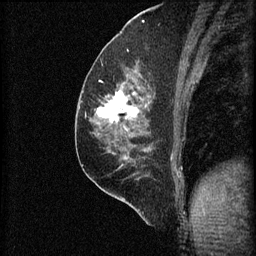
Breast MRI (dynamic contrast-enhanced), one sagittal slice; slice 33 of 60 in the series (ordered by position); 3 images stored at this slice position (order not interpretable as contrast timing); 1.5 T; TE 4.2 ms, TR 8.2 ms; 2 mm slice thickness; 256 × 256 image matrix, field of view 180 × 180 mm. Patient: female, 59 years.
Outlined on this slice (semi-automatic segmentation, software-assisted and operator-edited):
- analysis volume of interest (the breast-tissue region the enhancement analysis was run in; not a lesion): bounding box (x1, y1, x2, y2) in pixels: (92, 74, 154, 131)
- tumour enhancement mask (voxels above the 70 % enhancement threshold inside the analysis volume of interest): (97, 80, 141, 123)